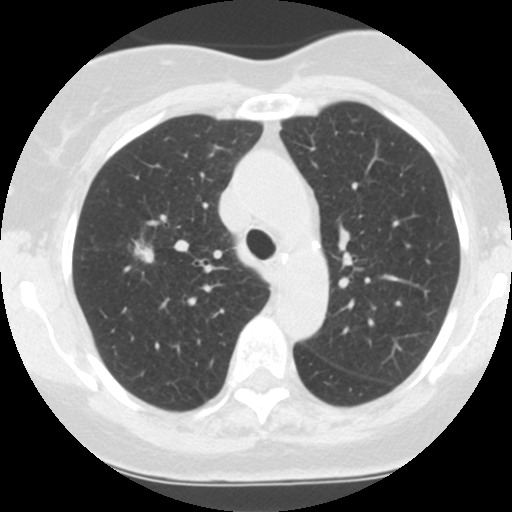
Low-dose screening chest CT, one axial slice; position 76 of 106 along the scan axis; 120 kVp; one of 2 acquisitions stored at this slice position; lung window (W 1500 / L -600 HU); 2.5 mm slice thickness; 512 × 512 image matrix.
Annotated regions visible in this slice (manually delineated by an expert):
- lesion 1 (tumor, upper lobe of right lung): bounding box <136,247,153,262> (left, top, right, bottom; pixels)